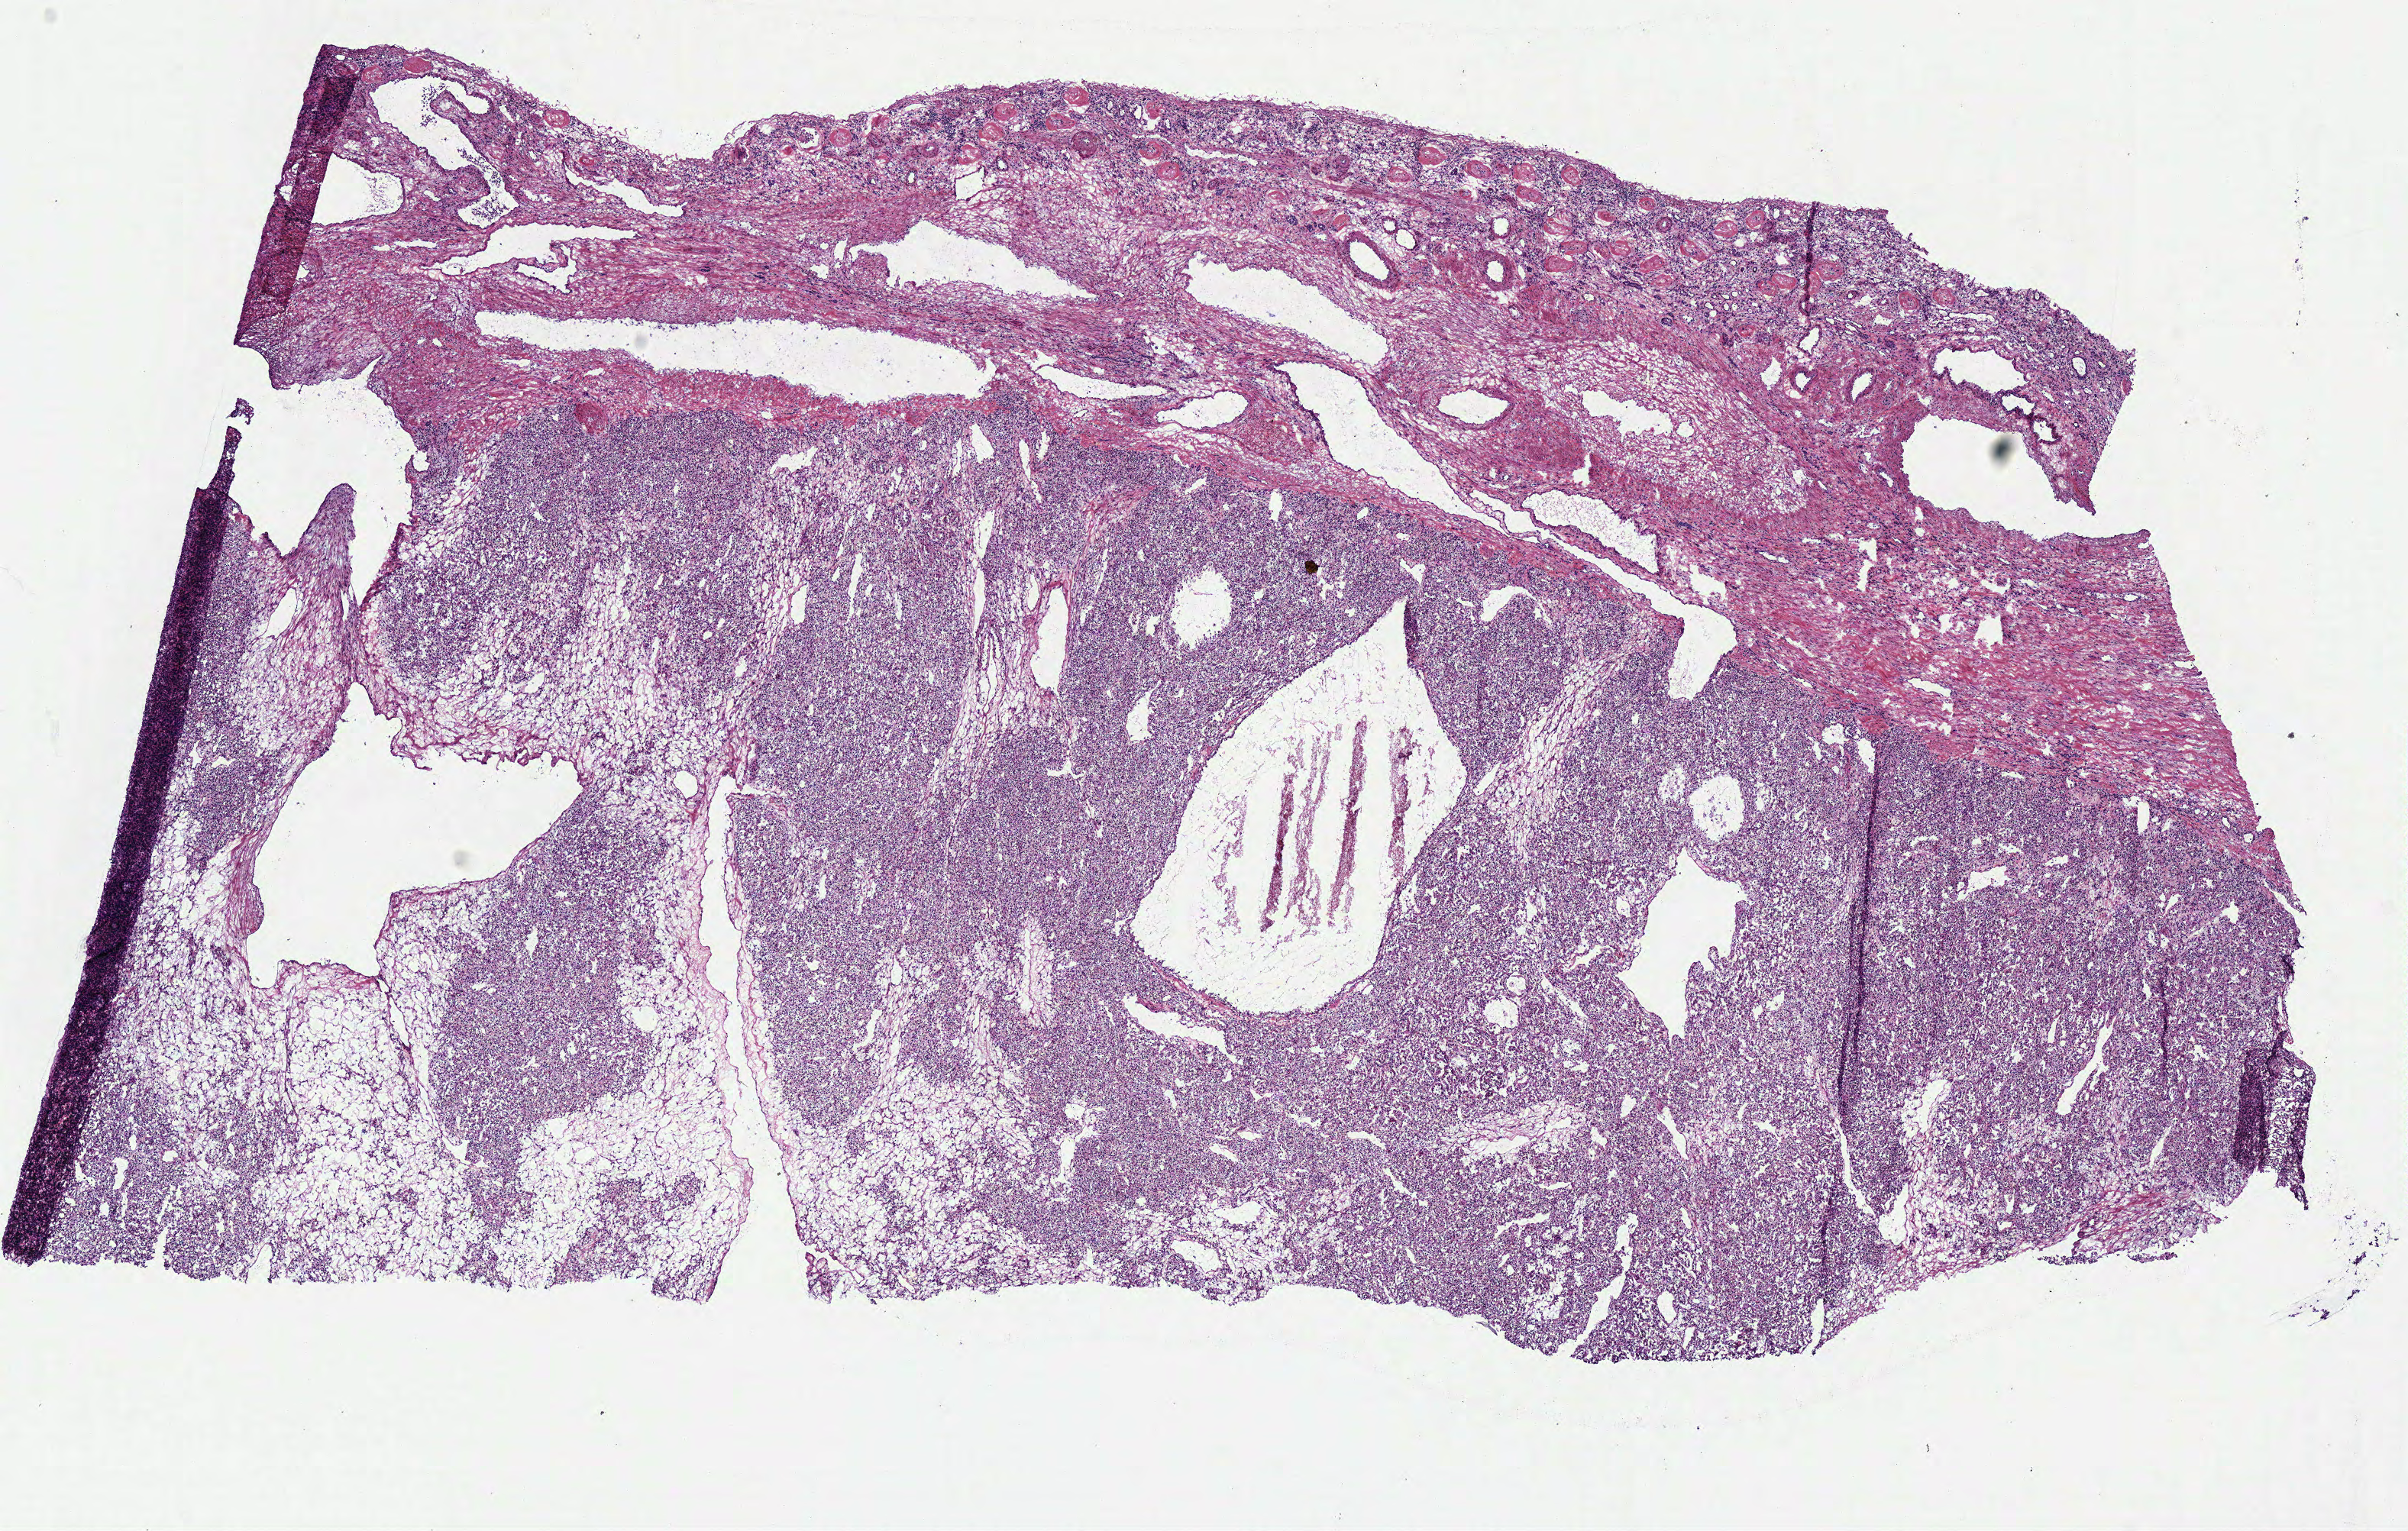
H&E whole-slide image — a low-resolution overview of the entire scanned area, about 12.4 x 7.9 mm; frozen section; kidney, primary tumour sample. Patient: male, age at initial diagnosis 60 years. Histologic grade: G2 (moderately differentiated). Pathologist review of this section (percent, as recorded): tumour cells 75%, tumour nuclei 80%, normal cells 10%, stromal cells 15%, necrosis 0%.
• histologic diagnosis: Clear cell adenocarcinoma, NOS
• AJCC pathologic stage: I
• lymph nodes positive (case pathology): 0 of 10 examined